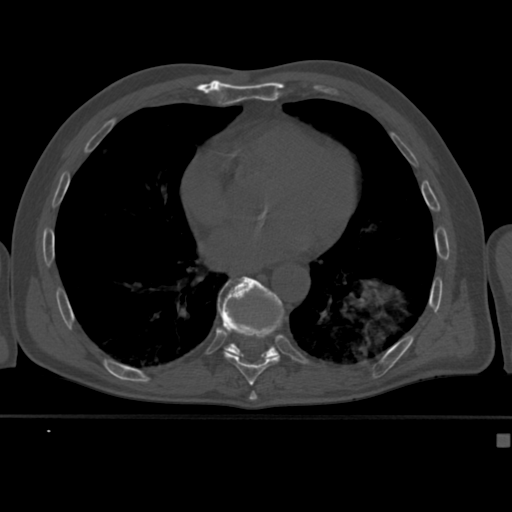
CT including the spine, one axial slice; reconstruction kernel Br40s; 120 kVp; bone window (W 1800 / L 400 HU); 512 × 512 image matrix, field of view 337 × 337 mm. Patient: male, 64 years. From the clinical record (not read from this slice): primary cancer: uterus; vertebrae with lytic lesions (as recorded): T1, T4, T5, T7, L5.
Annotated regions visible in this slice (semi-automatic segmentation, software-assisted and operator-edited):
- T10 vertebra: box from (x=218, y=276) to (x=285, y=362) px
- T9 vertebra: (x=218, y=278)–(x=283, y=382)